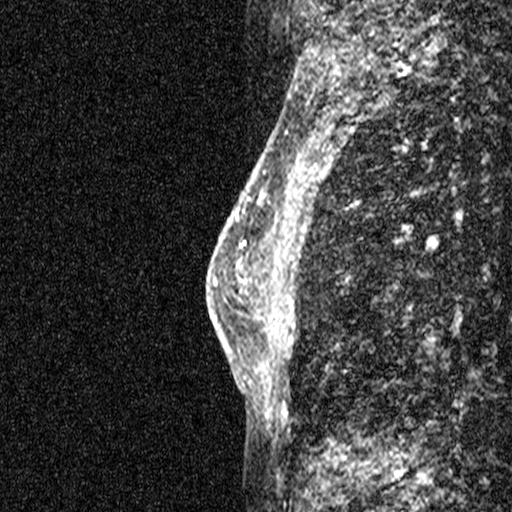
Breast MRI (dynamic contrast-enhanced), one sagittal slice. Position 23 of 44 along the scan axis. Dynamic contrast-enhanced study with each time point stored as its own series, time point 2 of 3 at this slice position (early post-contrast, ordered by acquisition time). 1.5 T. TE 4.5 ms, TR 11 ms. 512 × 512 image matrix, field of view 200 × 200 mm. Patient: female, 45 years. From the clinical record (not read from this slice): setting: breast cancer imaged before/during neoadjuvant chemotherapy; receptor status: HR-positive, HER2-negative.
Outlined on this slice (semi-automatic segmentation, software-assisted and operator-edited):
- analysis volume of interest (the breast-tissue region the enhancement analysis was run in; not a lesion): box from (x=256, y=218) to (x=351, y=359) px
- tumour enhancement mask (voxels above the 90 % enhancement threshold inside the analysis volume of interest): (x=286, y=302)–(x=295, y=323)